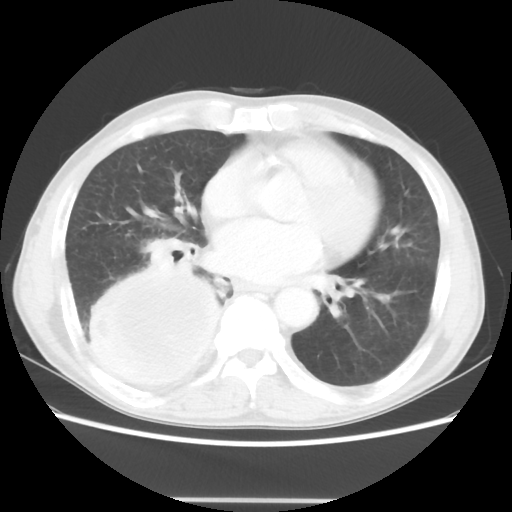
Chest CT, one axial slice. Slice 19 of 48 in the series (ordered by position). Reconstruction kernel STANDARD. Lung window (W 1500 / L -600 HU). 512 × 512 image matrix, field of view 361 × 361 mm. Patient: male, 66 years. From the clinical record (not read from this slice): clinical TNM (as recorded): T4 N1 M1; histopathological grade: G3.
Annotated regions visible in this slice (rectangle marked by the reading radiologist):
- lung tumour (recorded histology: small cell carcinoma): box from (x=88, y=263) to (x=232, y=391) px